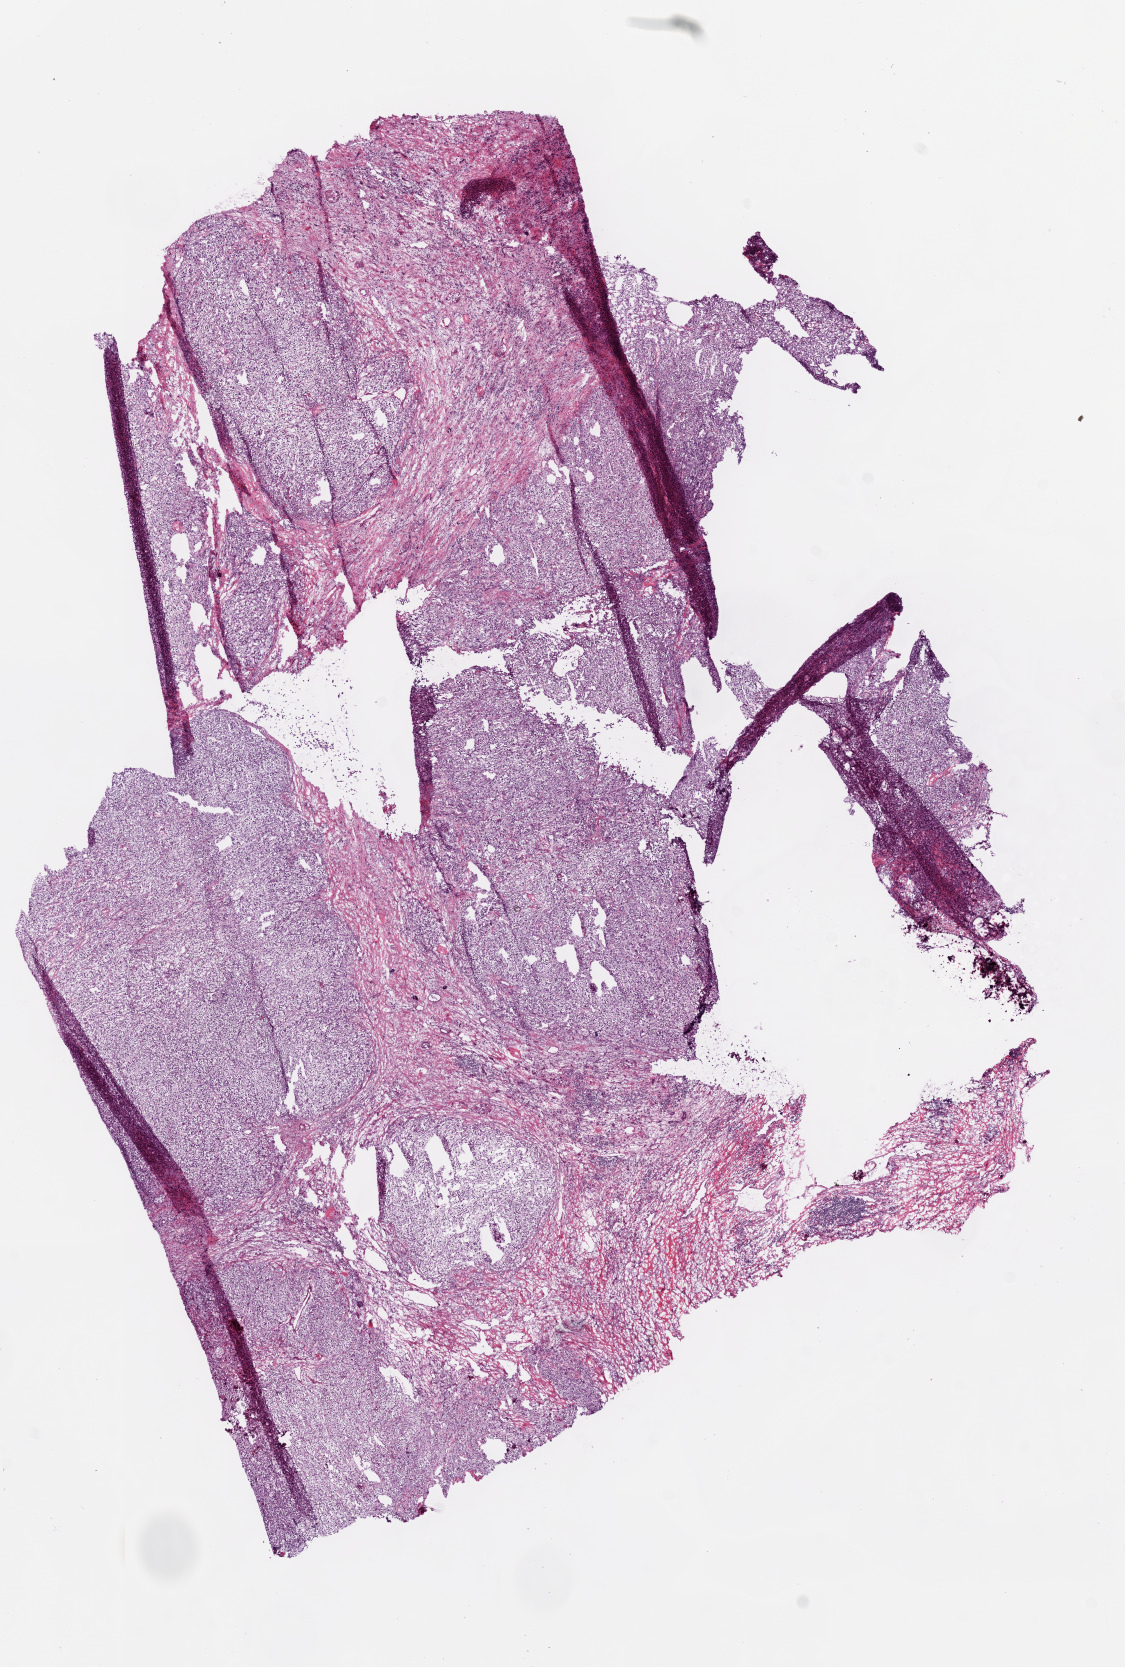
Digitized H&E tissue section (whole slide) — low-resolution overview of the scanned area, about 9.0 x 13.4 mm (slide scanned at 20x); frozen section; sample: primary tumour, kidney. Female, age 76 years at initial diagnosis. Histologic grade: G2 (moderately differentiated). Slide review estimates, as recorded: tumour cells 75%, tumour nuclei 70%, normal cells 20%, stromal cells 5%, necrosis 0%.
TNM: T1b N1 M0. AJCC pathologic stage: III. Lymph nodes positive (case pathology): 1 of 1 examined. Laterality: right. Pathologic diagnosis: Clear cell adenocarcinoma, NOS.